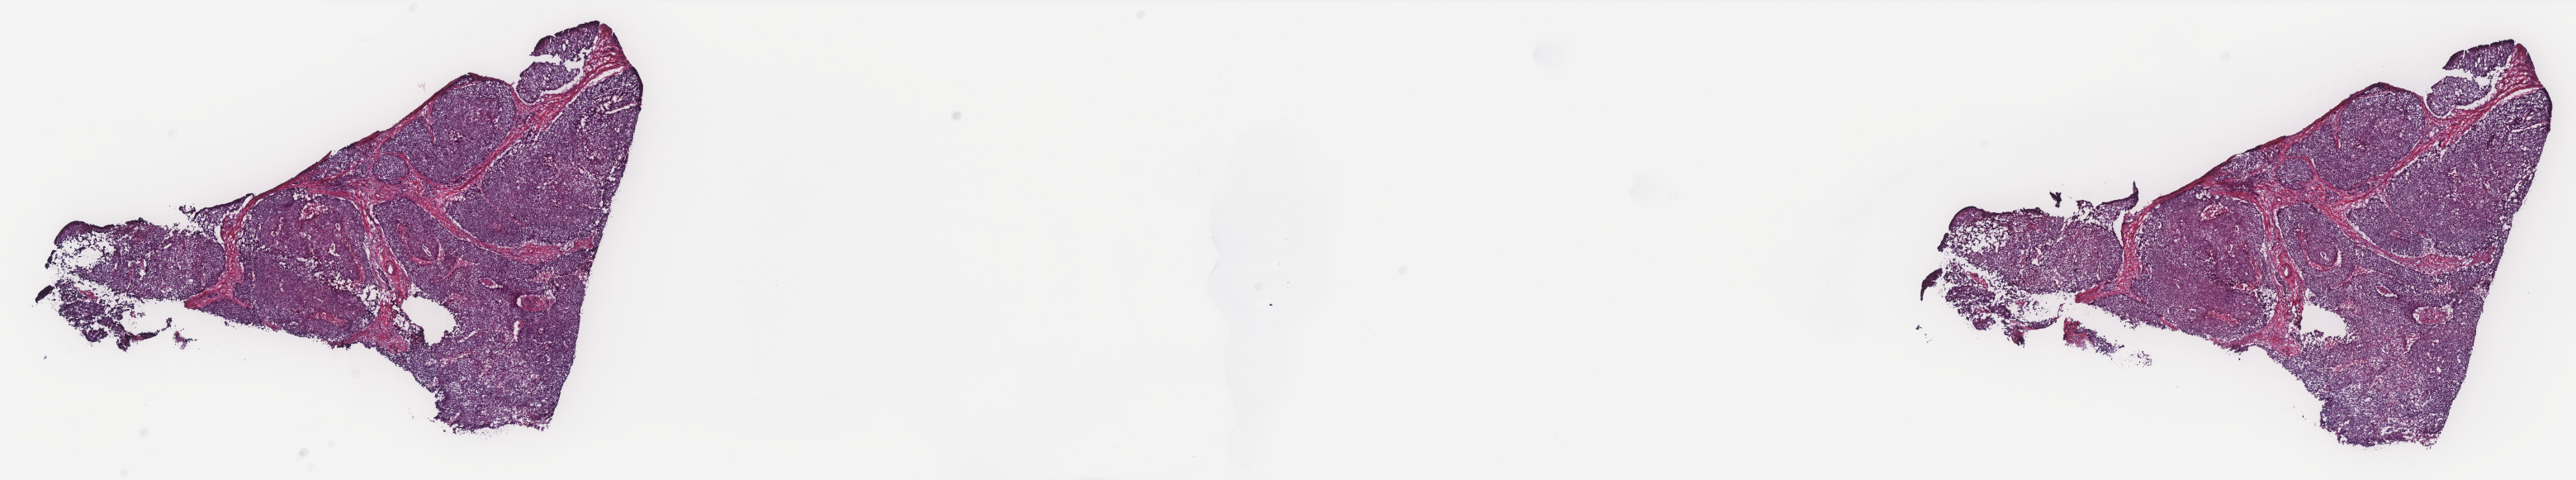
Whole-slide histology image, Hematoxylin and eosin (H&E) stained — whole scanned area (about 25.0 x 4.7 mm, from a 40x scan) shown as a low-resolution overview; frozen section from the top of the tissue portion; cervix, primary tumour sample. Female patient; age at initial diagnosis 43 years. Histologic grade: G2 (moderately differentiated). Composition of this section per pathologist review: tumour cells 83%, tumour nuclei 85%, normal cells 0%, stromal cells 15%, necrosis 2%. Inflammatory infiltration, as recorded: lymphocyte infiltration 5%, monocyte infiltration 2%, neutrophil infiltration 3%.
* lymph nodes positive (case pathology): 0 of 13 examined
* pathologic diagnosis: Squamous cell carcinoma, NOS (cervix uteri)
* FIGO stage: IB1